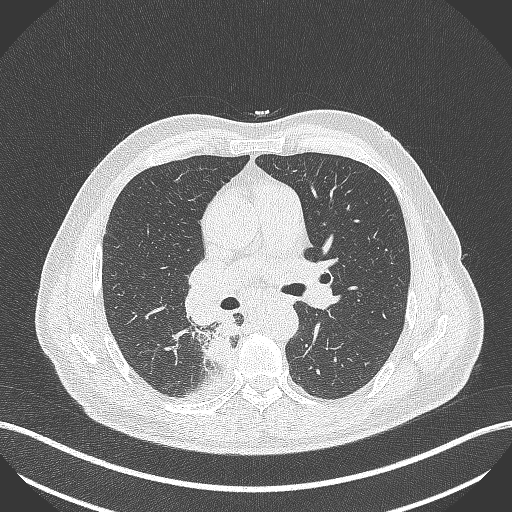
Chest CT, one axial slice. Slice 270 of 451 in the series (ordered by position). Reconstruction kernel B70f. Lung window (W 1500 / L -600 HU). 1 mm slice thickness. 512 × 512 image matrix. Patient: male, 61 years. Case-level facts recorded for this patient, not image findings: clinical TNM (as recorded): T1 N0 M0.
Outlined on this slice (bounding box drawn by a radiologist):
- lung tumour (recorded histology: small cell carcinoma): box from (x=201, y=321) to (x=244, y=367) px